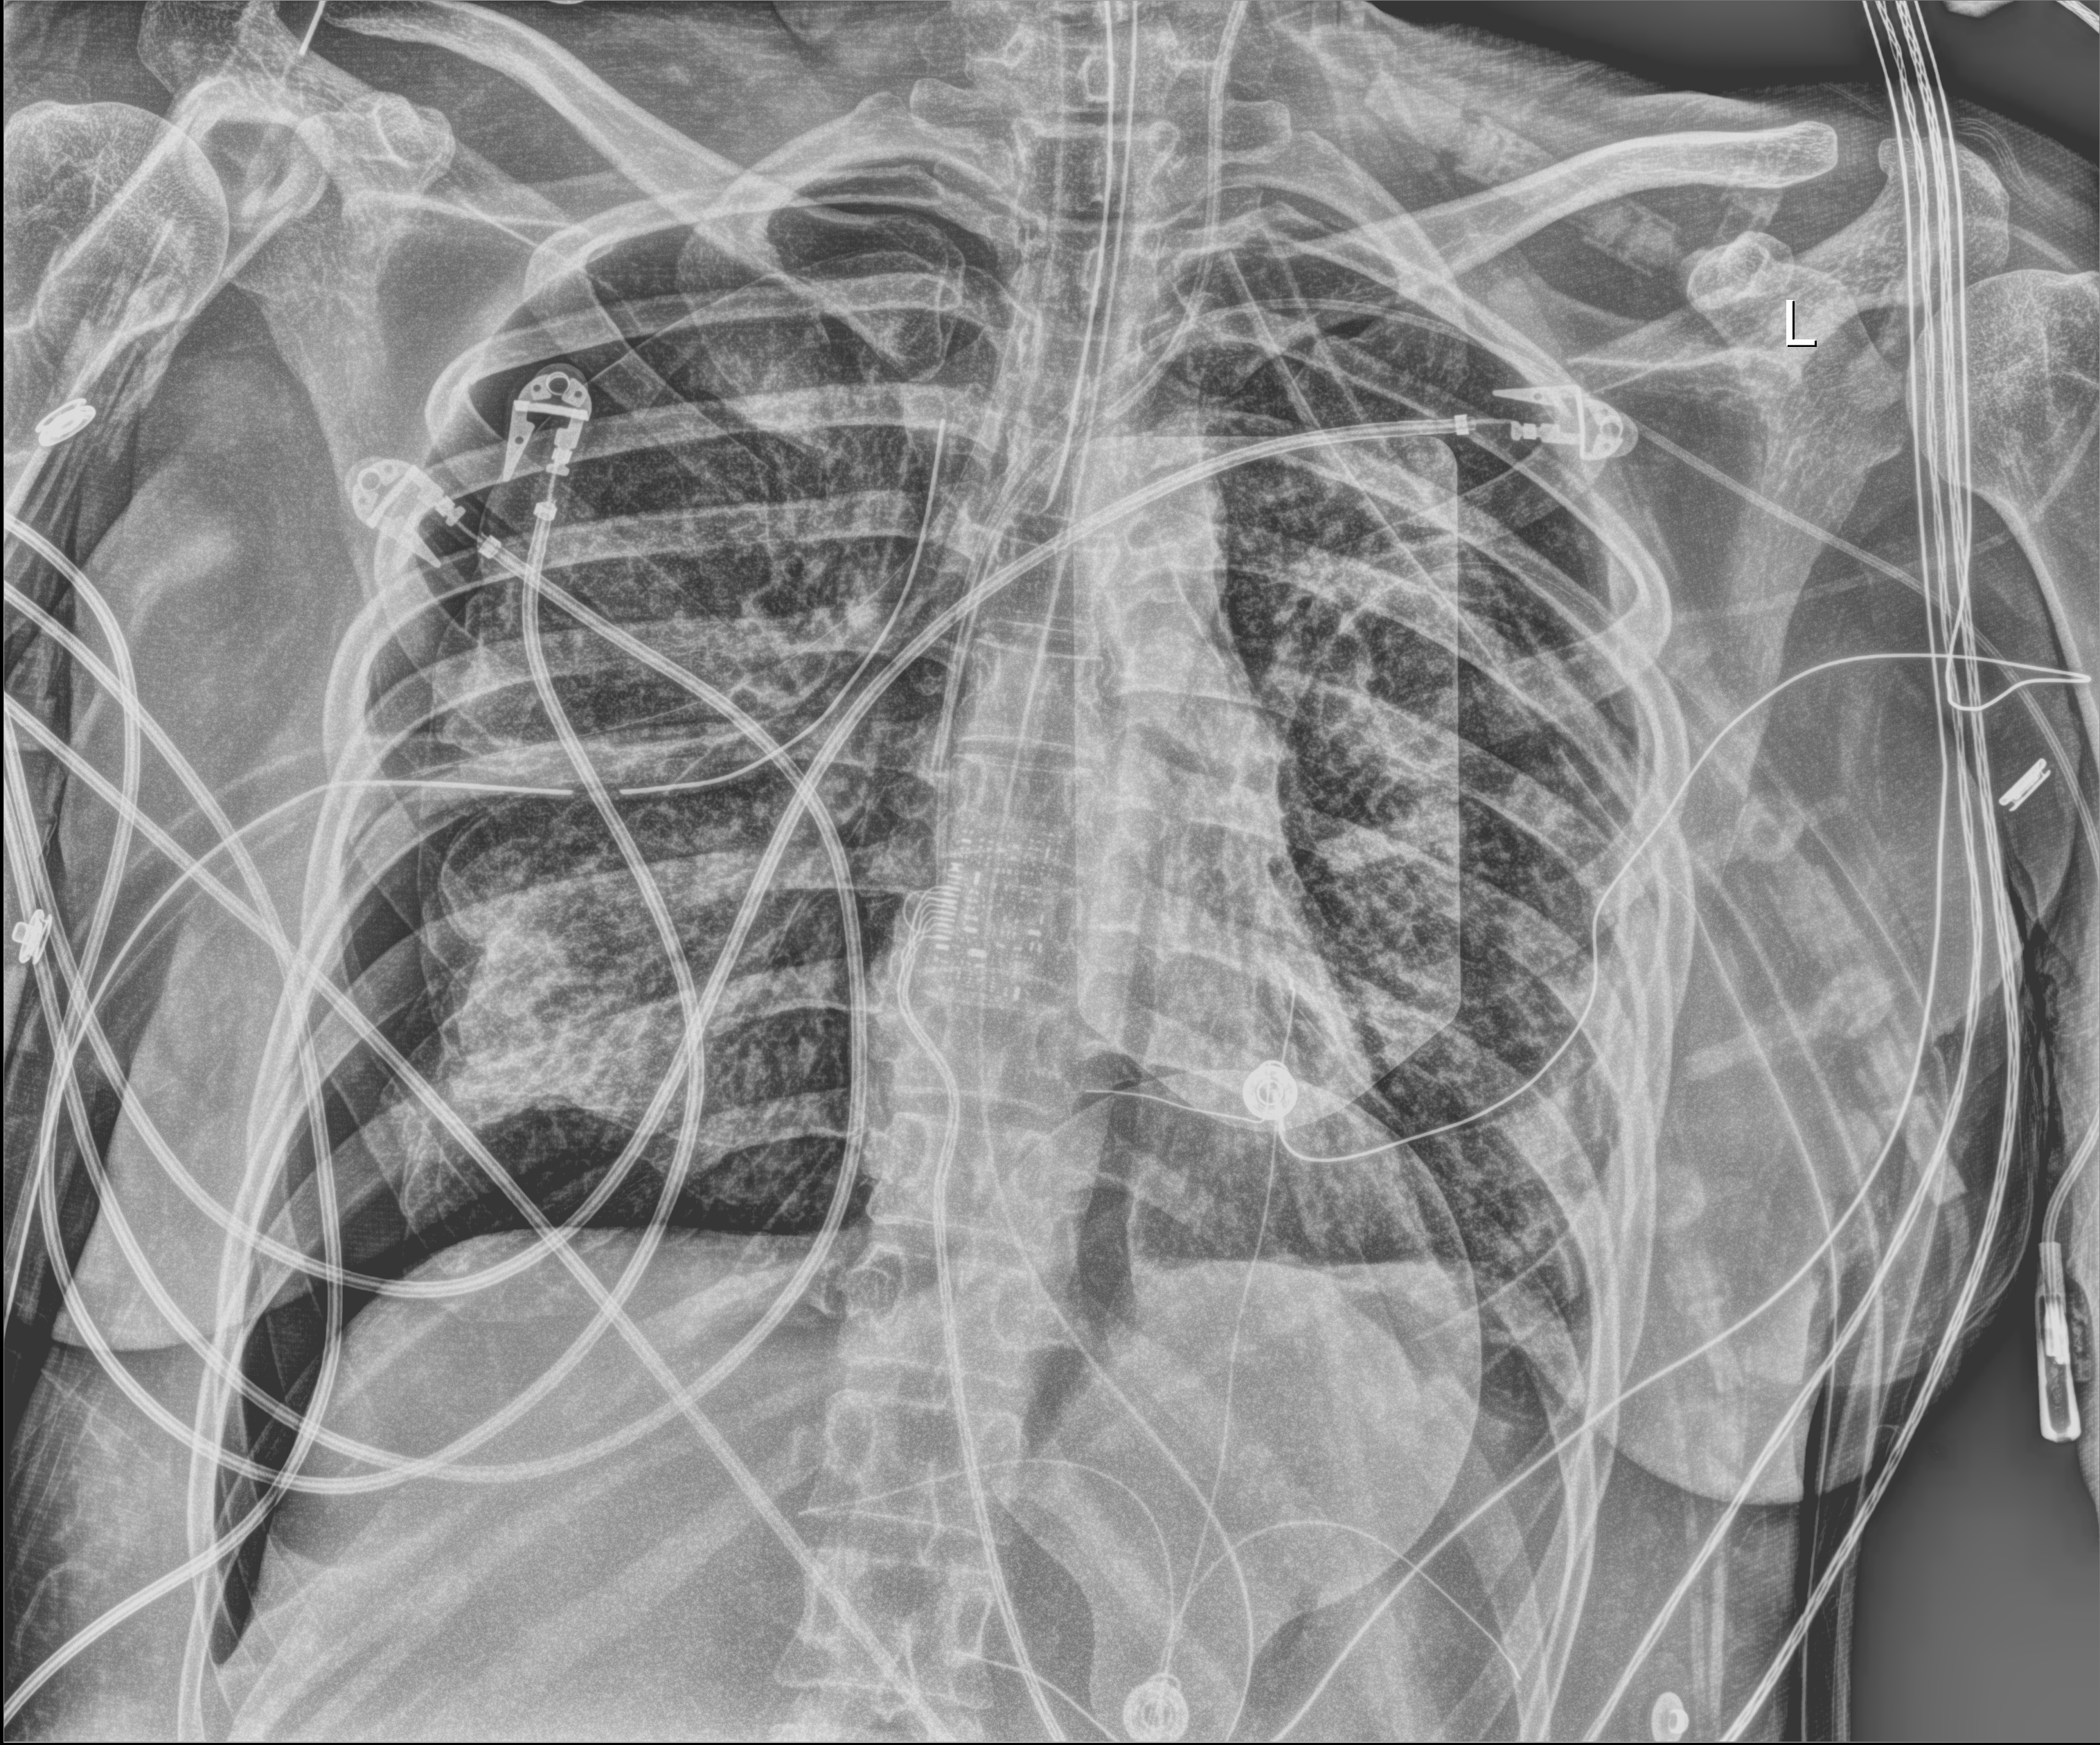
Portable chest radiograph, anteroposterior (AP) projection. Adult patient hospitalised with COVID-19, age 18–59 years.
From the hospital-stay record, not from the radiograph (when in the stay this image was taken is not recorded): mechanically ventilated during this hospital stay: yes.